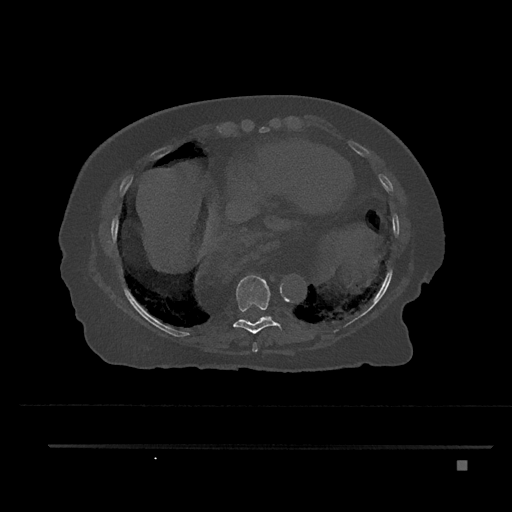
CT including the spine, one axial slice. Slice 397 of 797 in the series (ordered by position). Reconstruction kernel Br40s/3. 120 kVp. Bone window (W 1800 / L 400 HU). 0.5 mm slice thickness. 512 × 512 image matrix. Patient: female, 76 years. Case-level facts recorded for this patient, not image findings: primary cancer: lung.
Annotated regions visible in this slice (semi-automatic segmentation, software-assisted and operator-edited):
- T8 vertebra: bounding box [x1, y1, x2, y2] px = [252, 342, 258, 352]
- T9 vertebra: [233, 275, 283, 334]